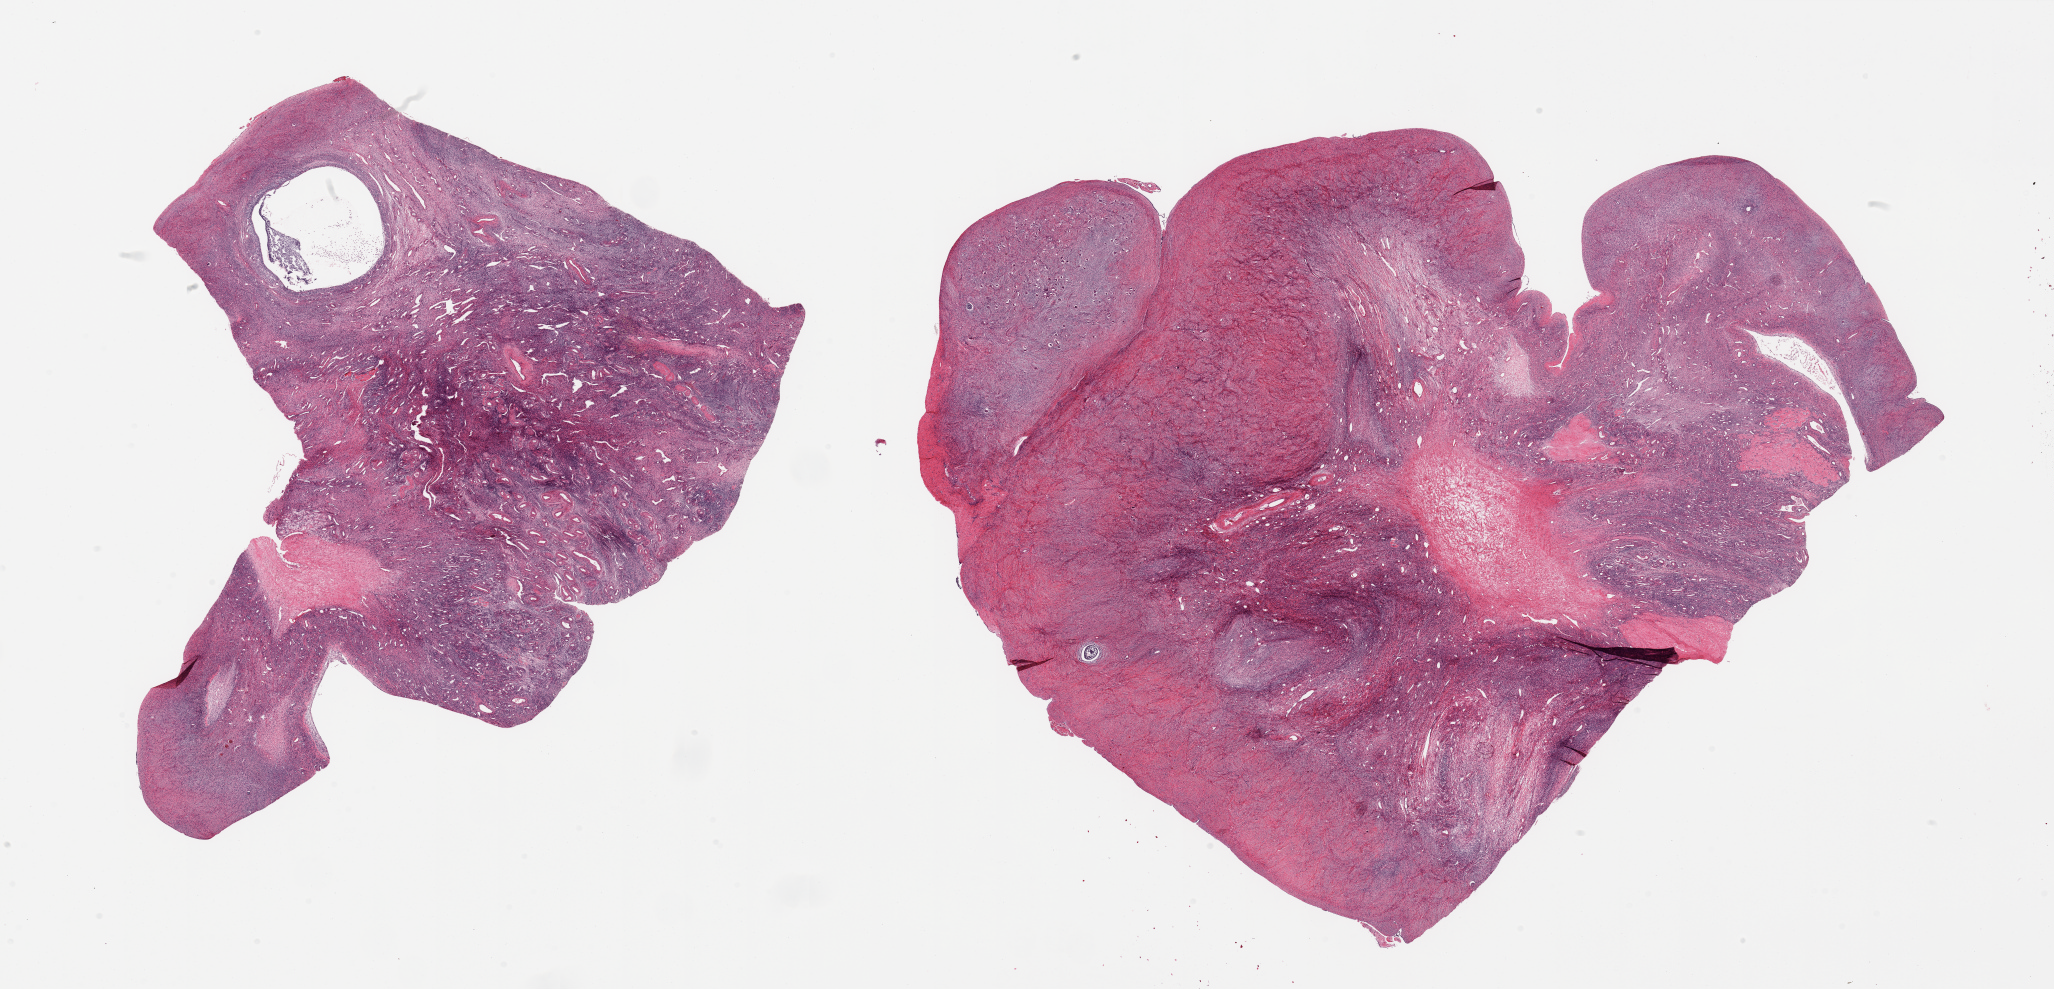
Digitized H&E-stained section — whole scanned area (about 32.5 x 15.6 mm, slide scanned at 20x) shown as a low-resolution overview; PAXgene-fixed paraffin-embedded (PFPE) section; sampled site (target tissue): ovary; donor tissue sample.
Reviewer comment on this tissue sample: 2 pieces.